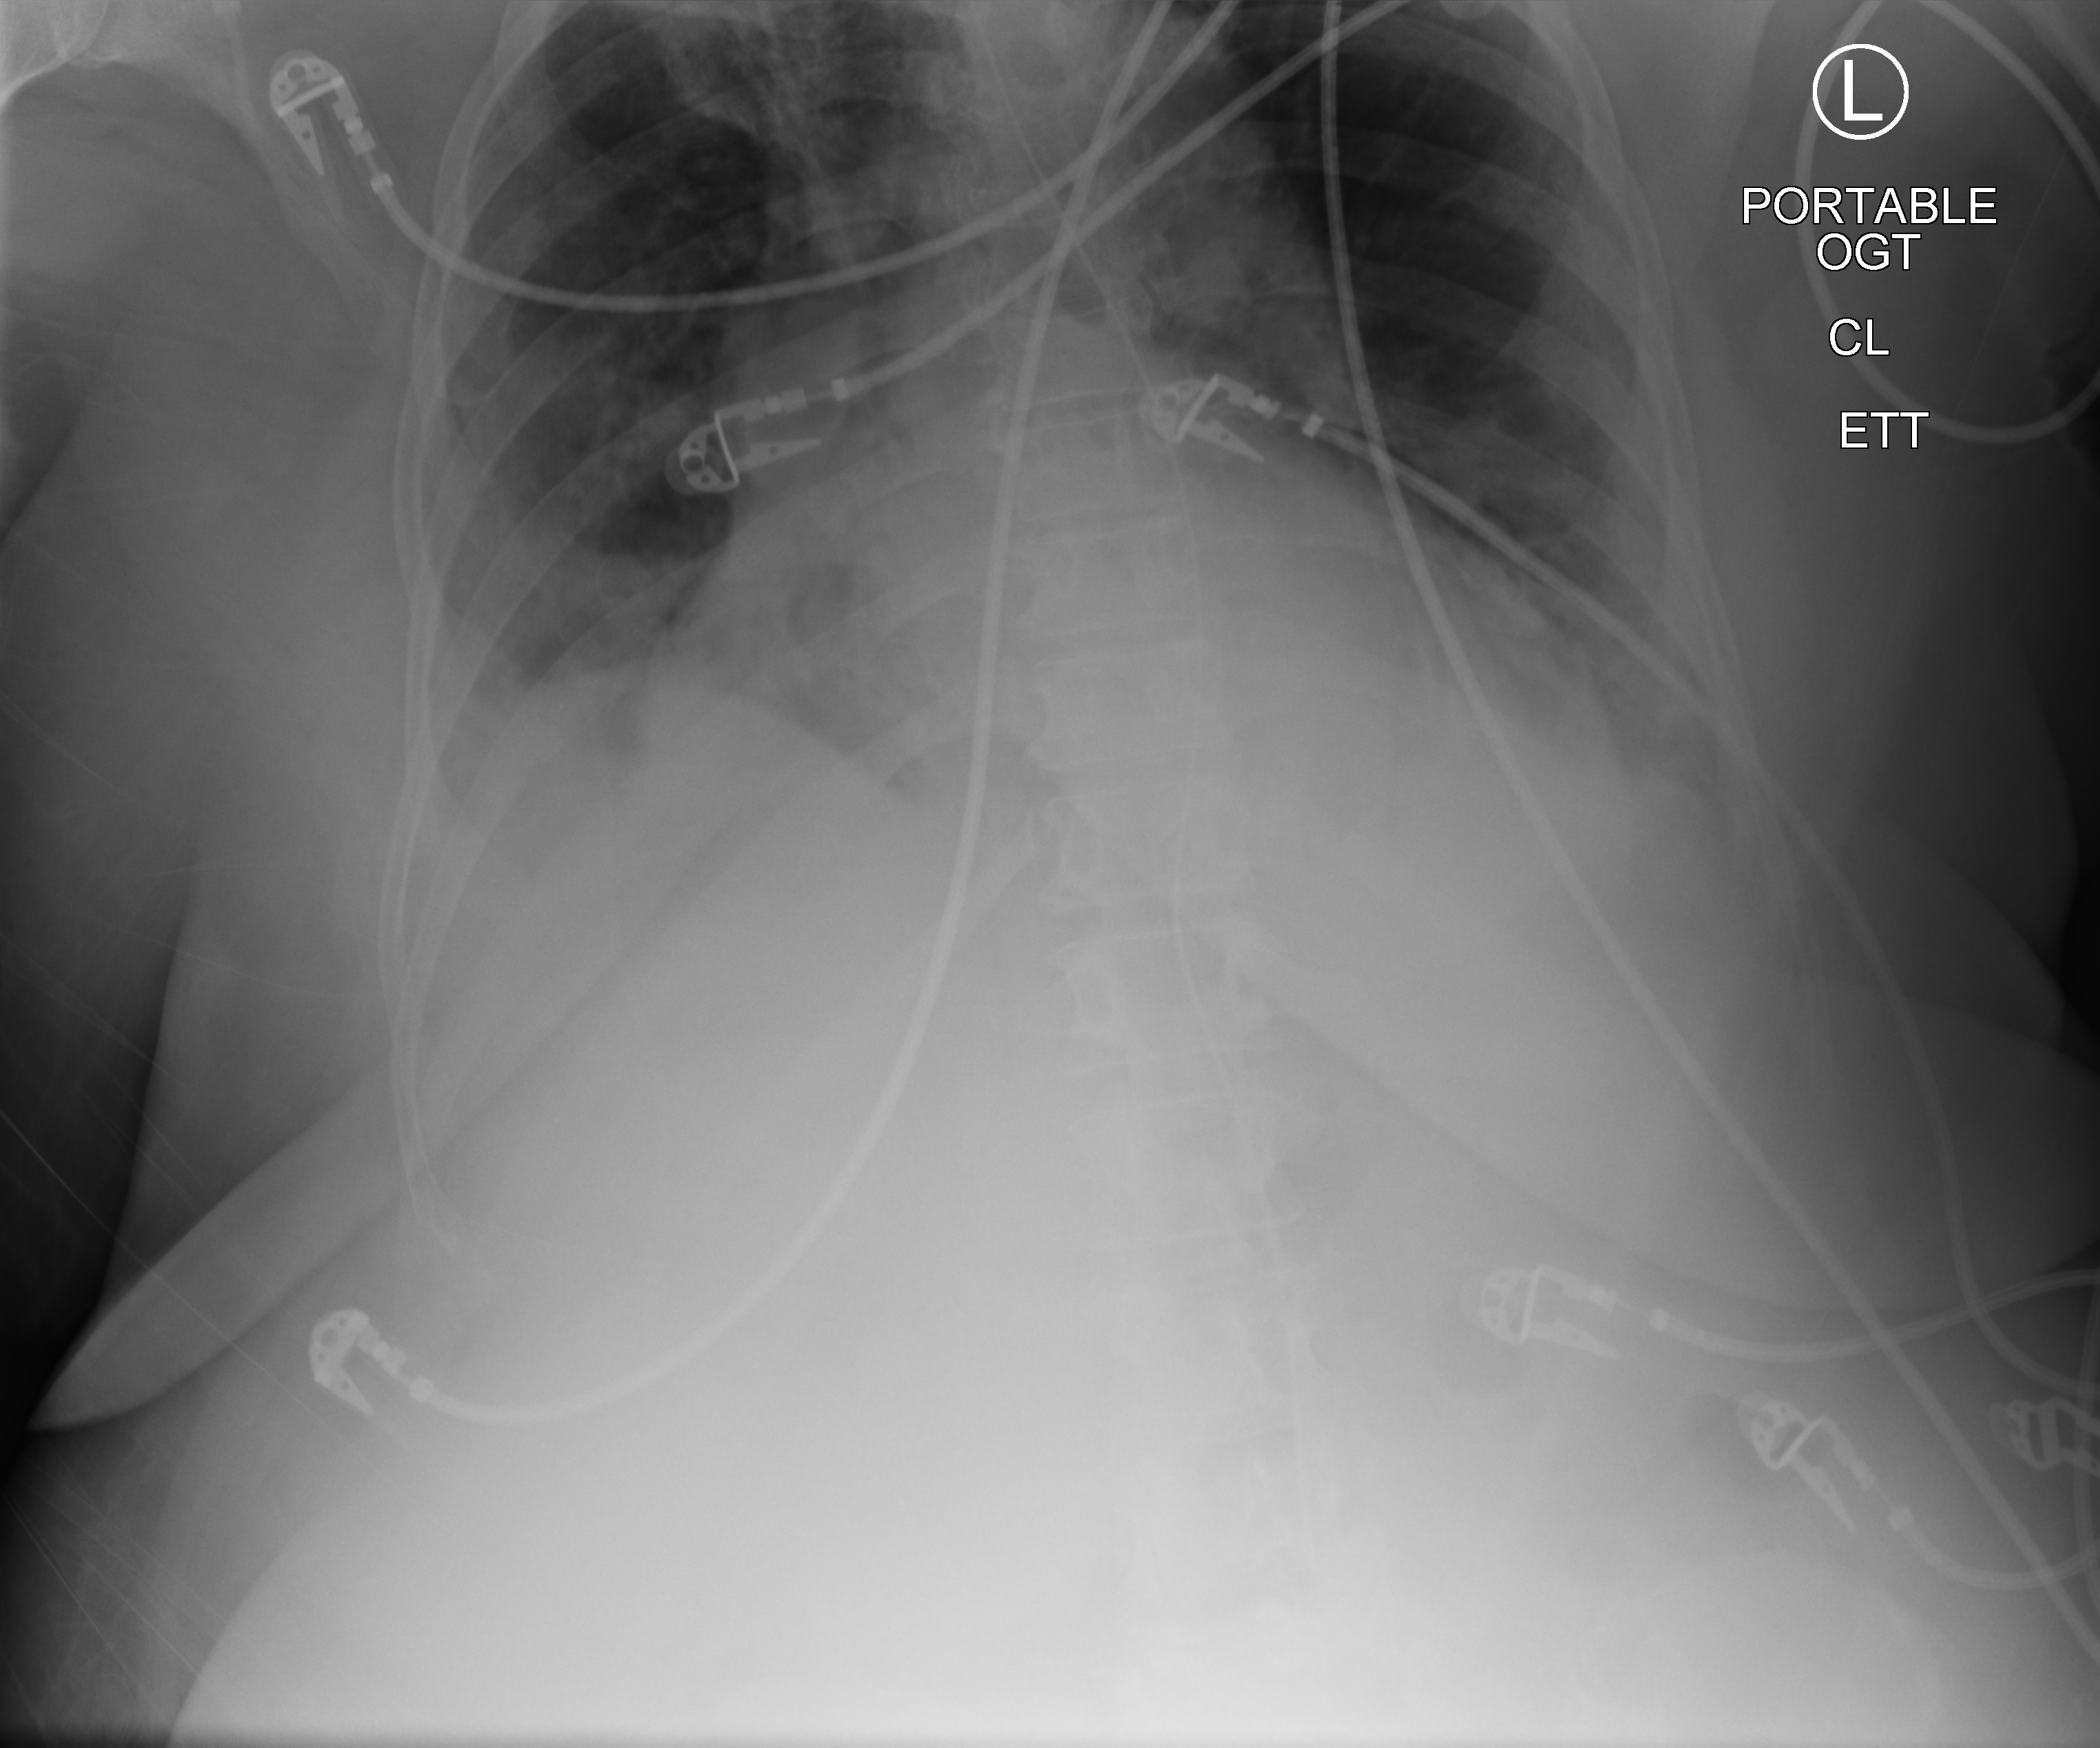
Portable chest radiograph, anteroposterior (AP) projection. Patient hospitalised with COVID-19; female, aged 60–74 years.
From the hospital-stay record, not from the radiograph (when in the stay this image was taken is not recorded): smoking status (admission record): never; length of hospital stay: 9 days.